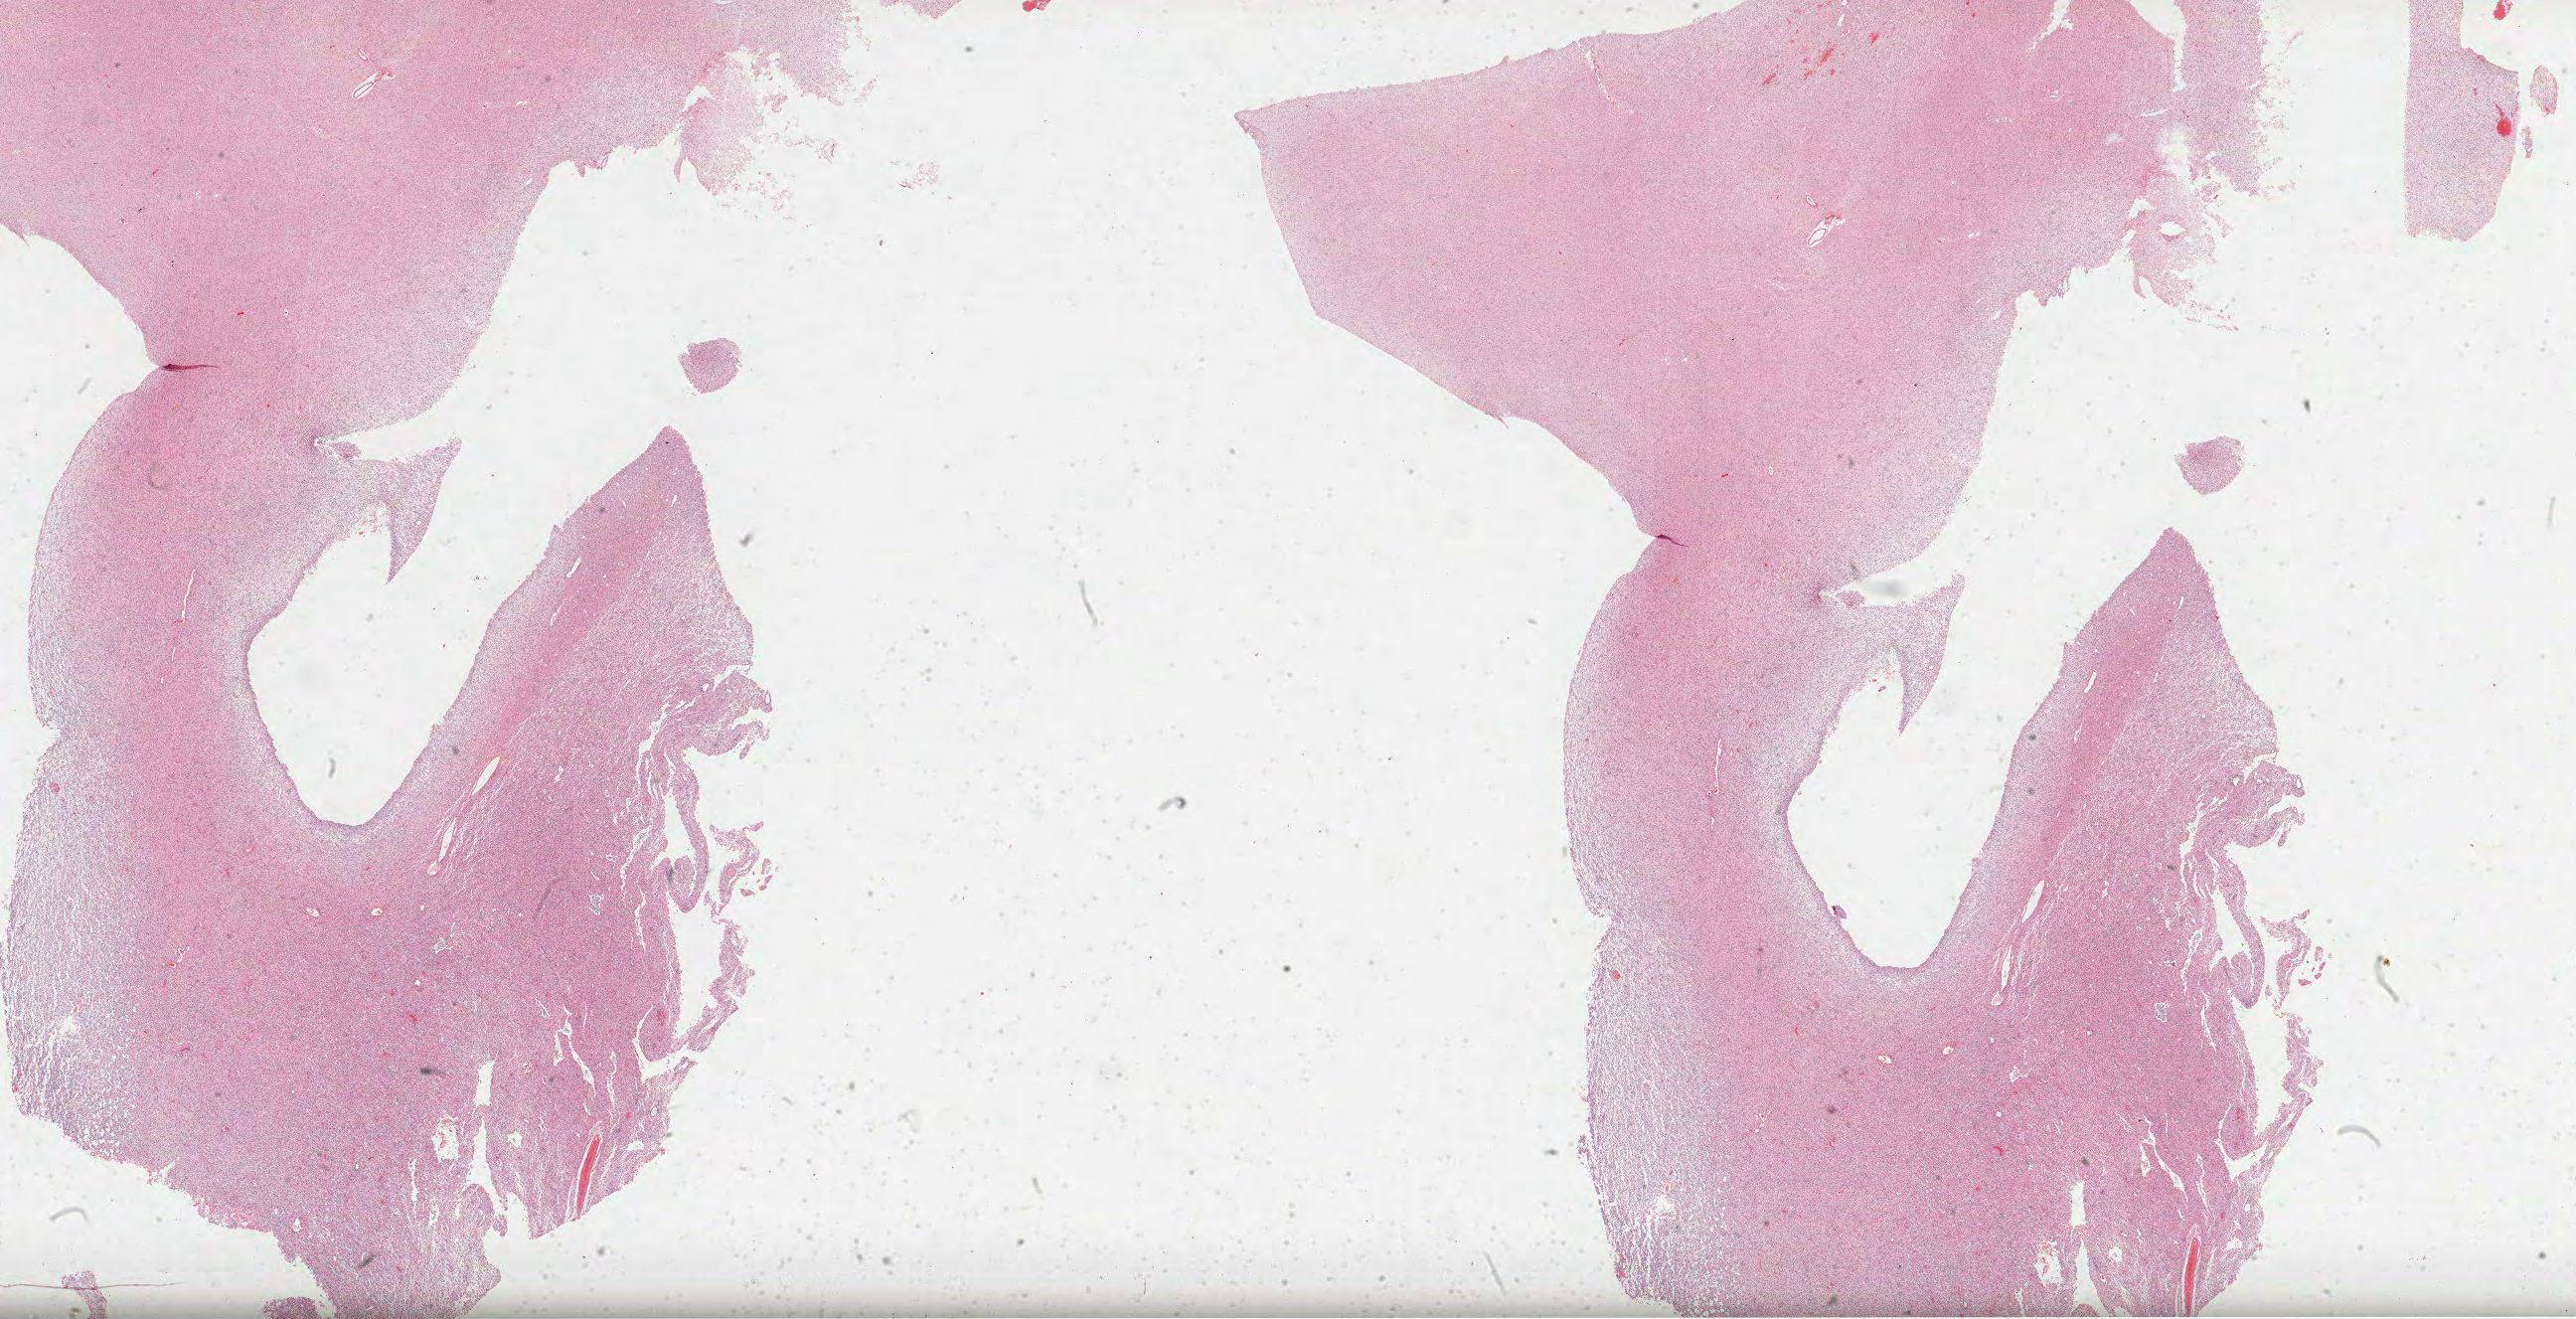
Hematoxylin and eosin (H&E) stained whole-slide image, low-resolution overview of the scanned area, about 41.8 x 21.4 mm (slide scanned at 40x); FFPE section; sample: primary tumour, brain. Patient: male, age at initial diagnosis 30 years. Histologic grade: G2 (moderately differentiated).
Diagnosis: Astrocytoma, NOS (cerebrum).